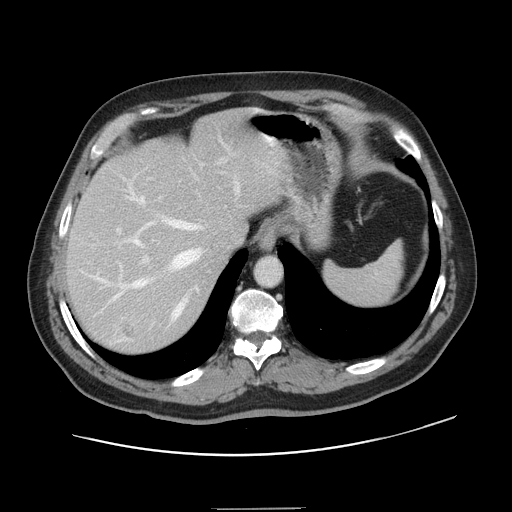
Contrast-enhanced abdominal CT, one axial slice; position 112 of 143 along the scan axis; 120 kVp; intravenous contrast given; soft-tissue window (W 400 / L 40 HU); 512 × 512 image matrix, field of view 402 × 402 mm. Male patient, age 62 years. Case-level facts recorded for this patient, not image findings: diagnosis: colorectal cancer liver metastases, imaged before liver resection.
Outlined on this slice (manually delineated by an expert):
- hepatic veins: bounding box <92,183,240,318> (left, top, right, bottom; pixels)
- liver: <67,114,283,353>
- planned liver remnant (the part of the liver to remain after resection): <67,114,283,280>
- portal vein (with intrahepatic branches): <103,159,222,342>
- liver metastasis: <122,324,138,339>